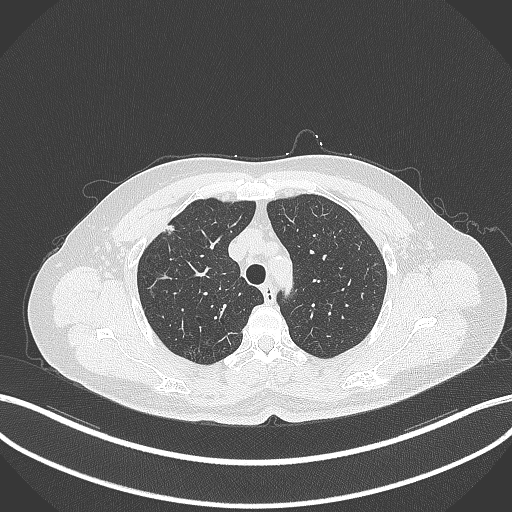
Chest CT, one axial slice; slice 288 of 353 in the series (ordered by position); lung window (W 1500 / L -600 HU); 512 × 512 image matrix. Patient: female, 56 years. Case-level facts recorded for this patient, not image findings: clinical TNM (as recorded): T1c N0 M0.
Structures marked on this image (rectangle marked by the reading radiologist):
- lung tumour (recorded histology: adenocarcinoma): bounding box [x1, y1, x2, y2] px = [157, 222, 179, 238]